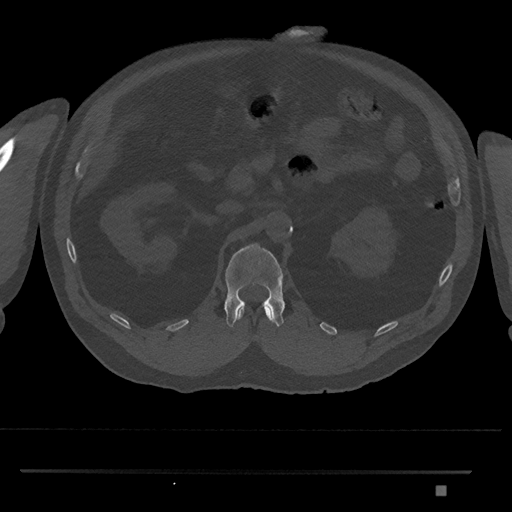
CT including the spine, one axial slice; reconstruction kernel Br40s/3; bone window (W 1800 / L 400 HU); 0.5 mm slice thickness; 512 × 512 image matrix, field of view 429 × 429 mm. Male patient, age 65 years. Case-level facts recorded for this patient, not image findings: primary cancer: prostate.
Annotated regions visible in this slice (semi-automatic segmentation, software-assisted and operator-edited):
- L1 vertebra: bounding box <224,243,285,327> (left, top, right, bottom; pixels)
- T12 vertebra: <236,308,271,321>